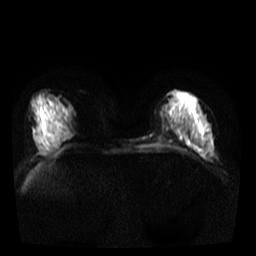
Breast MRI, one axial slice. Position 16 of 40 along the scan axis. Diffusion-weighted series; image 2 of 4 stored at this slice position (different b-values; order by instance number). 3 T. 5 mm slice thickness. 256 × 256 image matrix. Female patient.
Structures marked on this image (outlined manually by an expert reader):
- tumour on diffusion-weighted imaging: box from (x=204, y=144) to (x=212, y=156) px